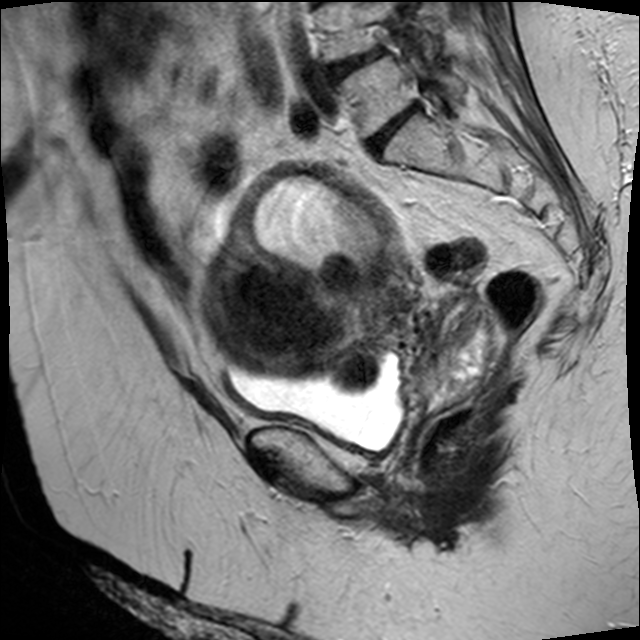
Pelvic MRI for cervical cancer, one sagittal slice. Position 26 of 45 along the scan axis. T2-weighted. 1.5 T. TE 89 ms, TR 4610 ms. 640 × 640 image matrix, field of view 260 × 260 mm. Female patient, age 50 years.
Structures marked on this image (expert manual segmentation):
- uterus and cervix: bounding box [x1, y1, x2, y2] px = [201, 162, 499, 408]